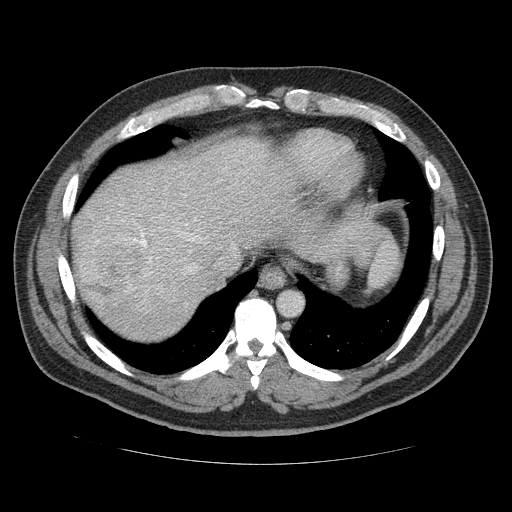
Contrast-enhanced abdominal CT (liver protocol), one axial slice; position 102 of 113 along the scan axis; reconstruction kernel STANDARD; 120 kVp; soft-tissue window (W 400 / L 40 HU); 512 × 512 image matrix, field of view 400 × 400 mm. Case-level facts recorded for this patient, not image findings: diagnosis: hepatocellular carcinoma (patient treated with transarterial chemoembolisation; whether this scan precedes or follows treatment is not stated here); TNM stage (as recorded): Stage-II; Child-Pugh class: B; tumour nodularity: multinodular.
Outlined on this slice (semi-automatically segmented with operator editing):
- abdominal aorta: bounding box [x1, y1, x2, y2] px = [279, 292, 302, 316]
- liver parenchyma outside the tumour (the mass and vessels are separate outlines, so this box may not span the whole liver): [74, 142, 290, 336]
- mass: [74, 213, 169, 297]
- liver vessels: [92, 231, 153, 265]